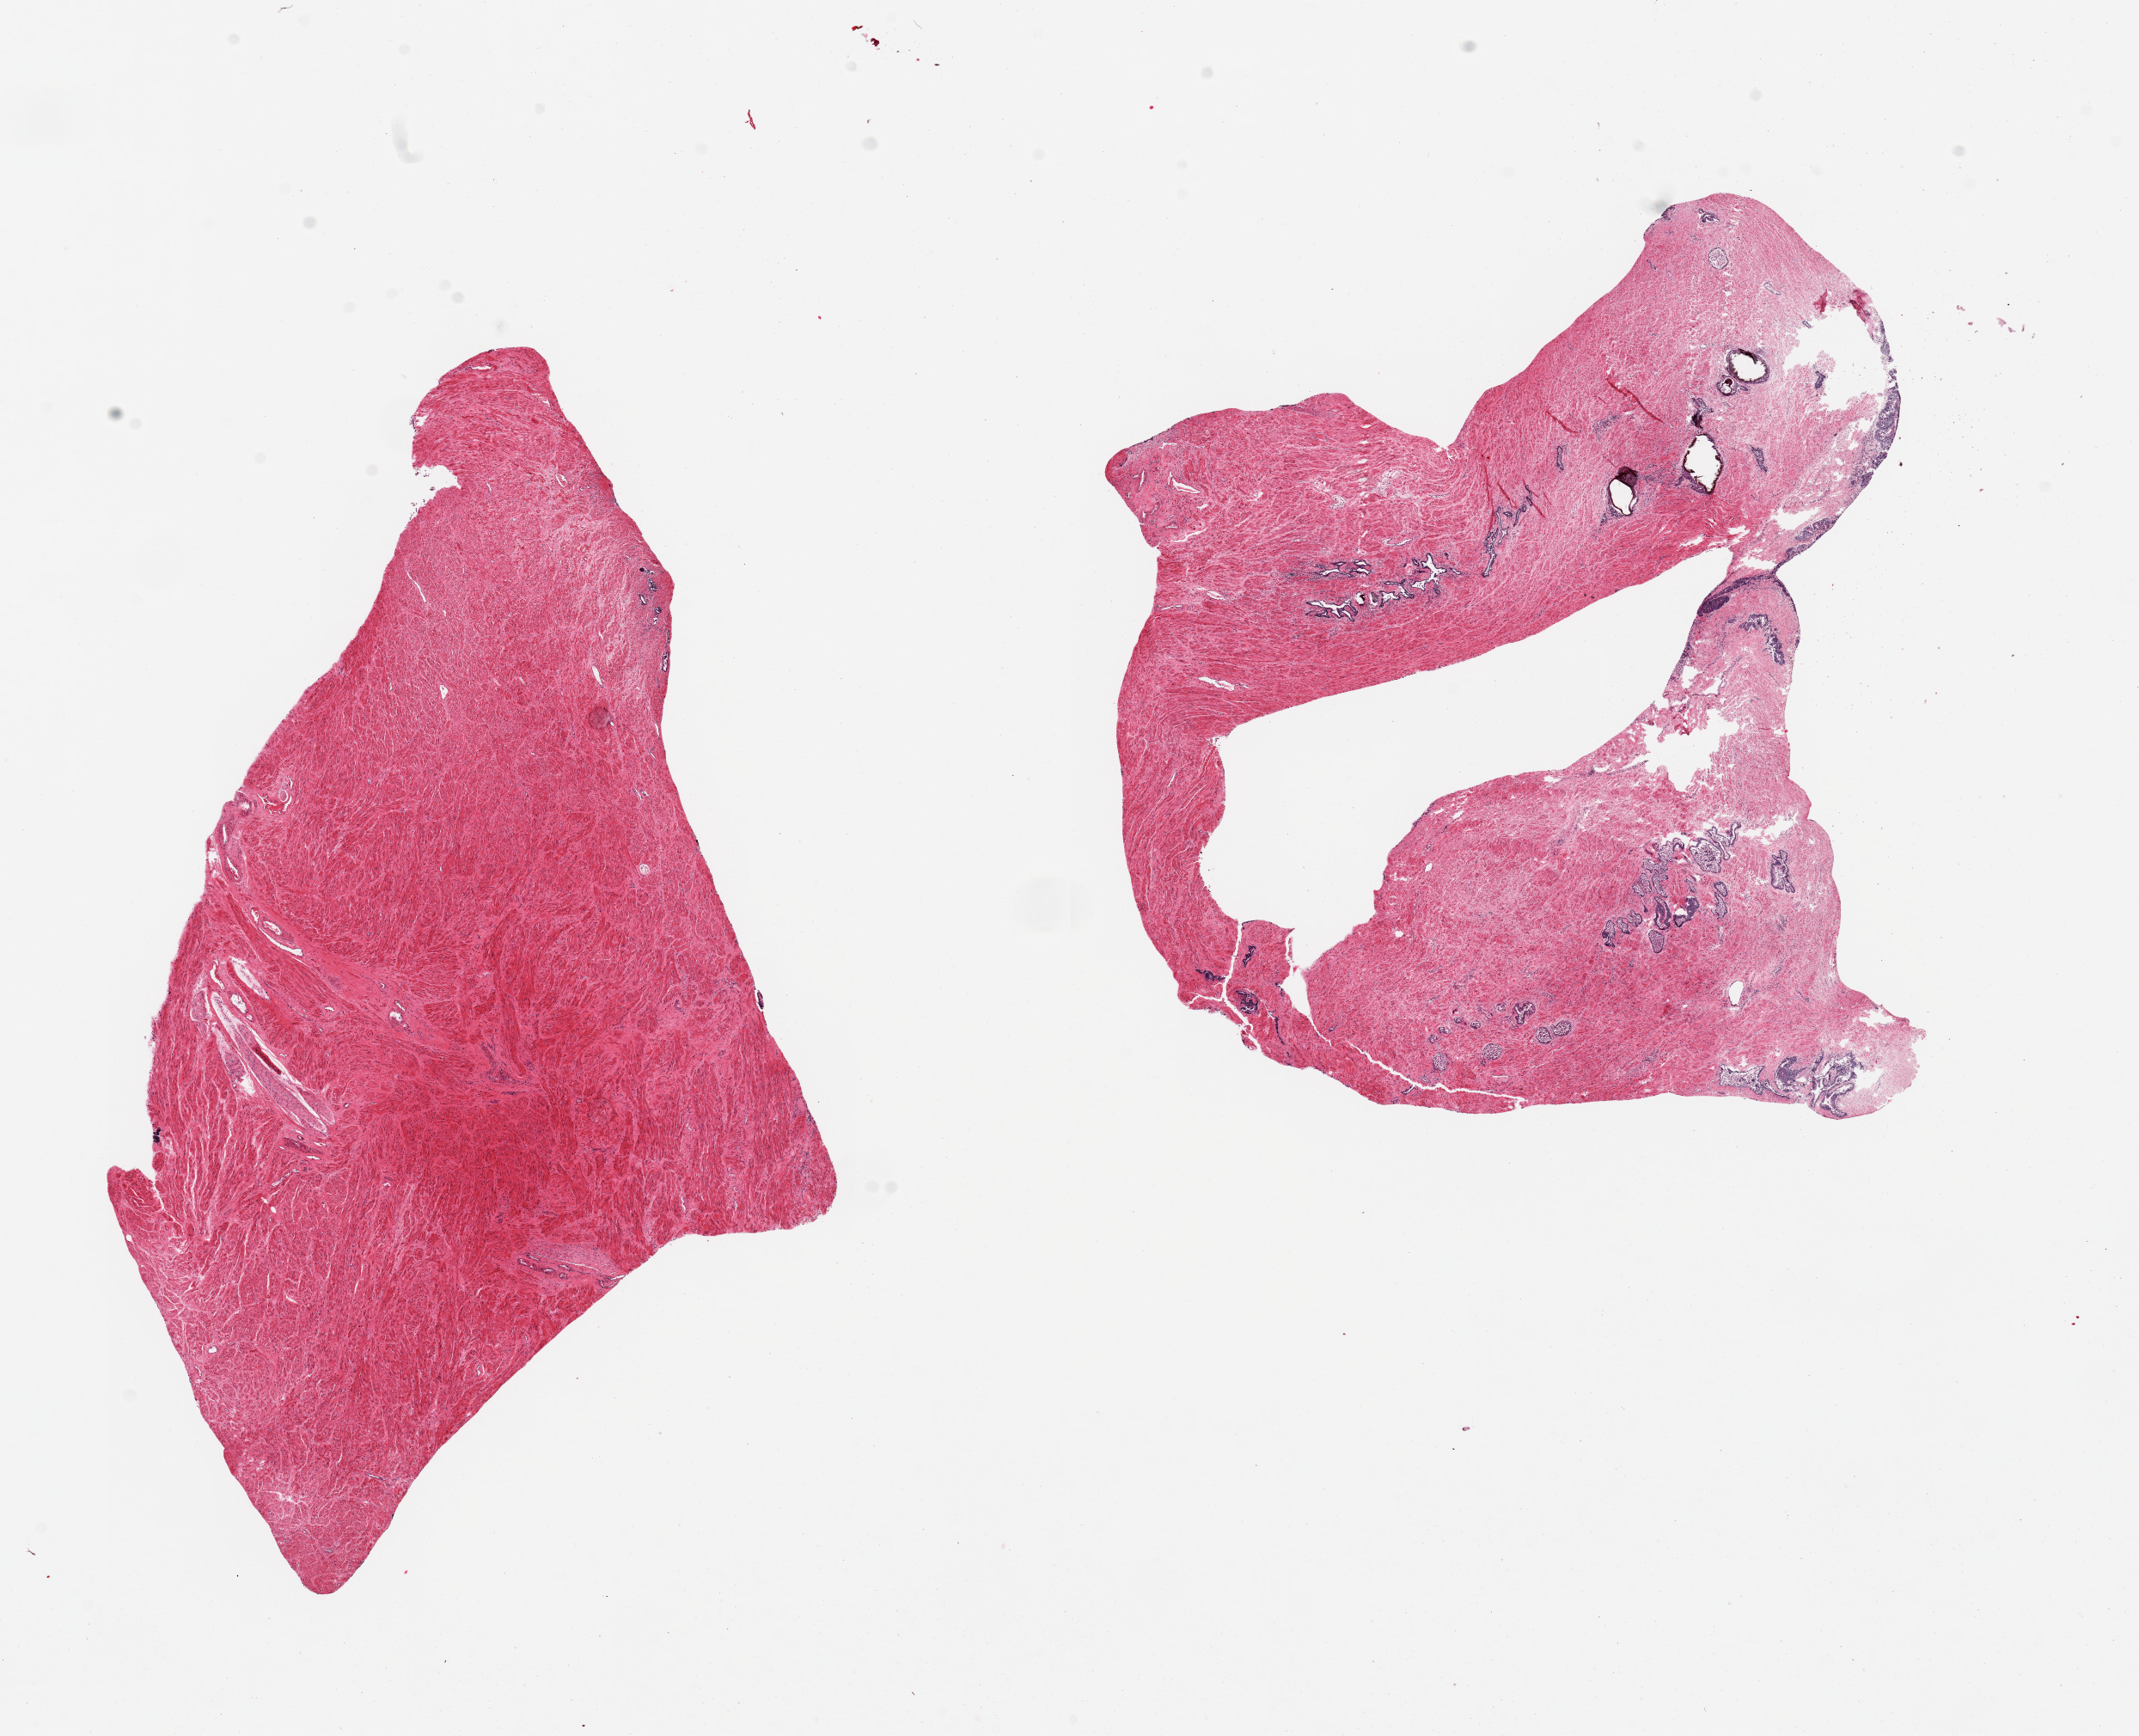
Digitized H&E-stained section, low-resolution overview of the scanned area, about 19.7 x 16.0 mm; PAXgene-fixed, paraffin-embedded tissue; section of prostate (target tissue); donor tissue sample. Donor: male.
Pathologist's review note for this sample: 2 pieces, mainly stroma, trace glands, moderately advanced autolysis.